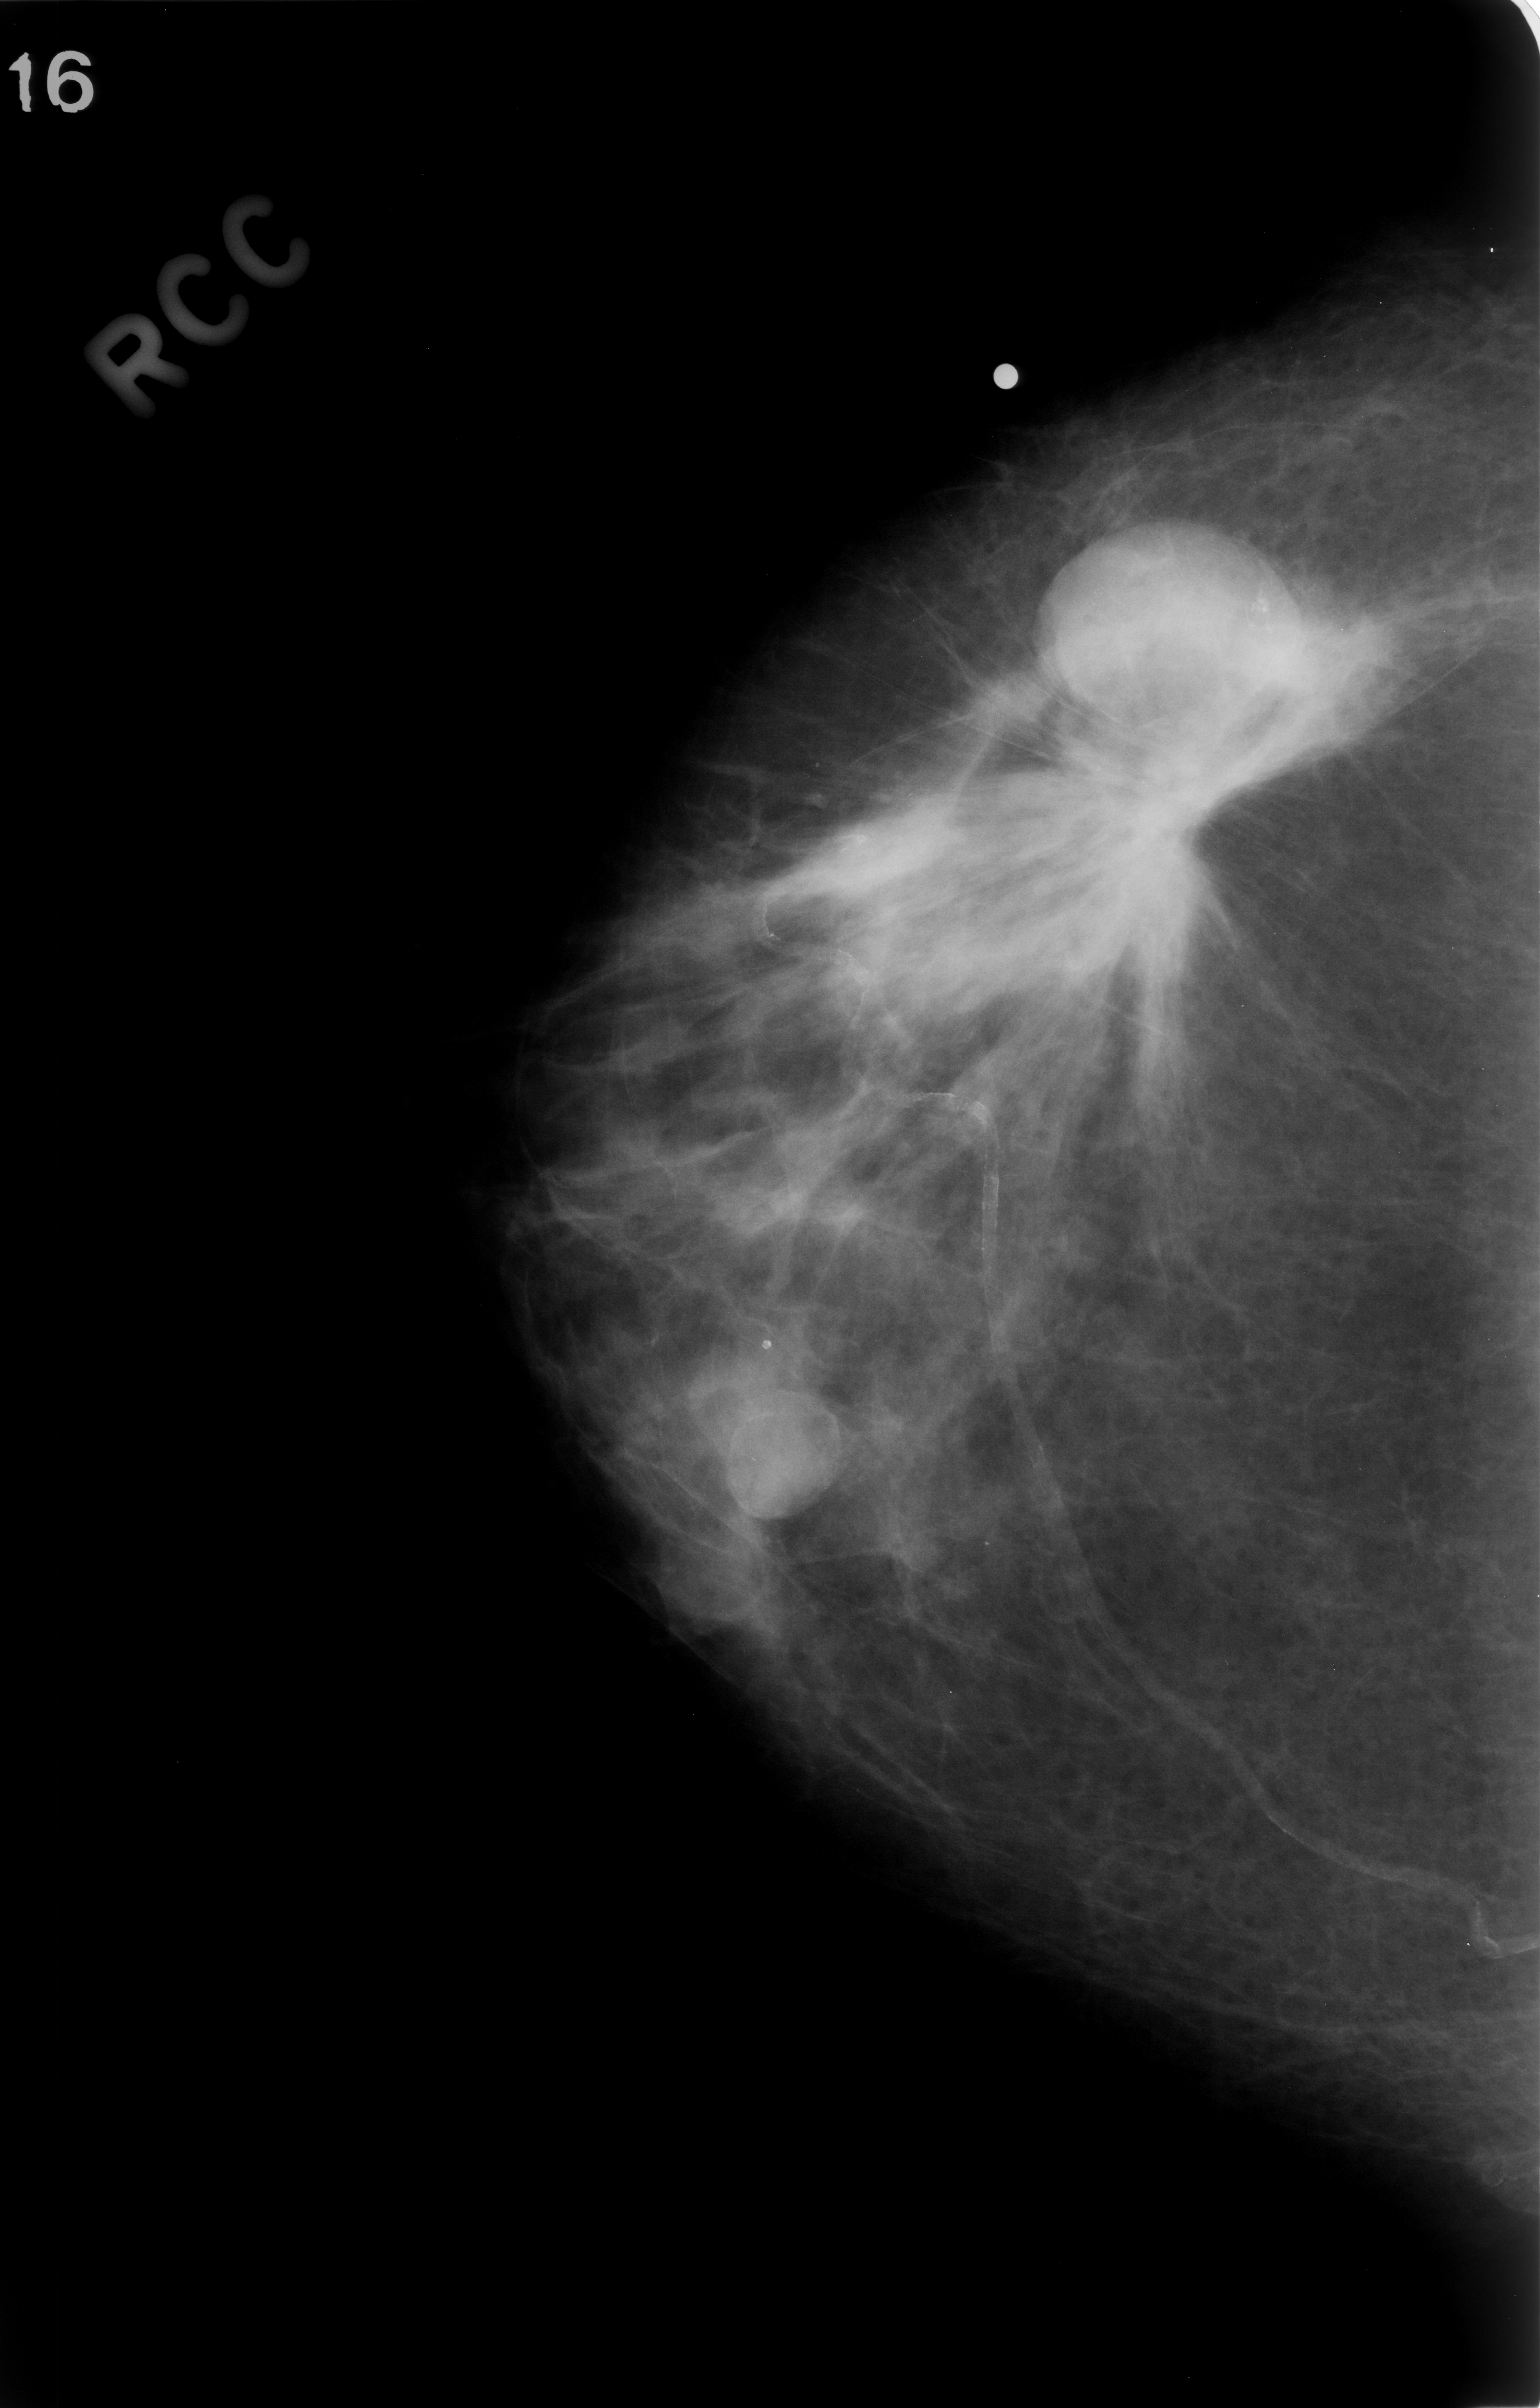
Mammogram (digitized film). Right breast. Craniocaudal (CC) view. Breast composition: scattered fibroglandular densities (BI-RADS density category 2 of 4). 1540 × 2408 image matrix.
Expert-marked regions of interest on this film, with their recorded descriptors:
- mass, shape irregular, margins spiculated; BI-RADS assessment category 5; pathology (as recorded): malignant: box from (x=929, y=591) to (x=1326, y=995) px